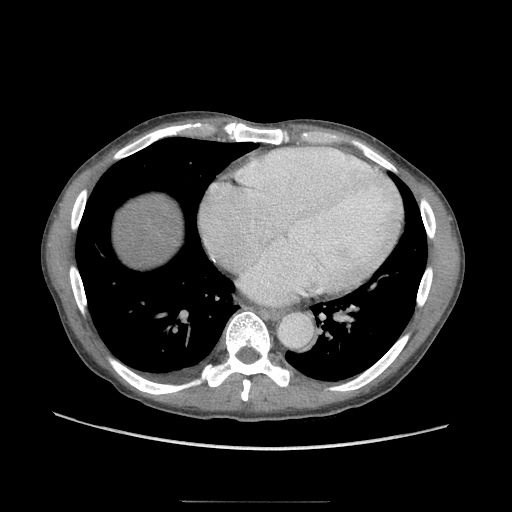
Contrast-enhanced abdominal CT (liver protocol), one axial slice; position 100 of 103 along the scan axis; soft-tissue window (W 400 / L 40 HU); 2.5 mm slice thickness; 512 × 512 image matrix. Case-level facts recorded for this patient, not image findings: diagnosis: hepatocellular carcinoma (patient treated with transarterial chemoembolisation; whether this scan precedes or follows treatment is not stated here); TNM stage (as recorded): Stage-IIIA; Child-Pugh class: A; tumour differentiation: moderately differentiated.
Annotated regions visible in this slice (semi-automatically segmented with operator editing):
- abdominal aorta: bounding box <278,312,312,346> (left, top, right, bottom; pixels)
- liver parenchyma outside the tumour (the mass and vessels are separate outlines, so this box may not span the whole liver): <122,204,172,254>